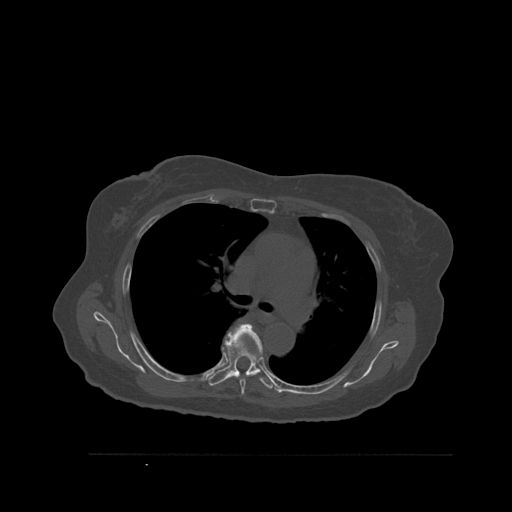
CT including the spine, one axial slice. Position 387 of 527 along the scan axis. Bone window (W 1800 / L 400 HU). 512 × 512 image matrix, field of view 470 × 470 mm. Patient: female, 73 years. Case-level facts recorded for this patient, not image findings: primary cancer: breast; vertebrae with lytic lesions (as recorded): L2.
Annotated regions visible in this slice (semi-automatic segmentation, software-assisted and operator-edited):
- T5 vertebra: bounding box <227,324,262,396> (left, top, right, bottom; pixels)
- T6 vertebra: <208,321,275,389>